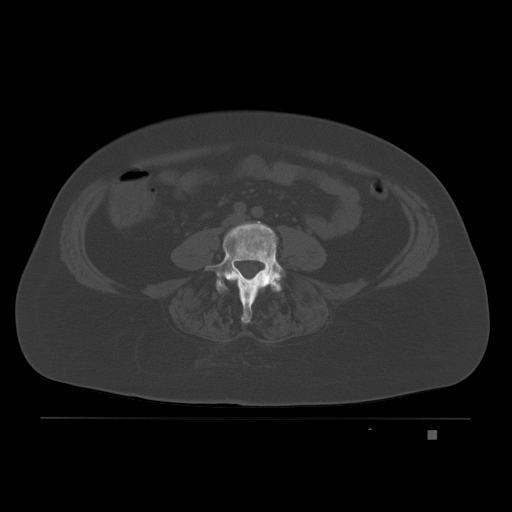
CT including the spine, one axial slice; slice 41 of 221 in the series (ordered by position); bone window (W 1800 / L 400 HU); 512 × 512 image matrix, field of view 474 × 474 mm. Patient: female, 63 years. Case-level facts recorded for this patient, not image findings: primary cancer: breast.
Outlined on this slice (semi-automatic segmentation, software-assisted and operator-edited):
- L3 vertebra: box from (x=231, y=278) to (x=235, y=281) px
- L4 vertebra: (x=206, y=221)–(x=286, y=324)